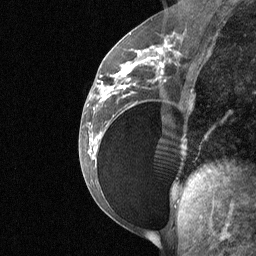
Breast MRI (dynamic contrast-enhanced), one sagittal slice; slice 30 of 64 in the series (ordered by position); dynamic contrast-enhanced study with each time point stored as its own series, time point 2 of 3 at this slice position (early post-contrast, ordered by acquisition time); 1.5 T; TE 4.8 ms, TR 27 ms; 2 mm slice thickness; 256 × 256 image matrix, field of view 200 × 200 mm. Female patient, age 34 years. From the clinical record (not read from this slice): setting: breast cancer imaged before/during neoadjuvant chemotherapy; receptor status: HR-positive, HER2-negative.
Outlined on this slice (semi-automatically segmented with operator editing):
- analysis volume of interest (the breast-tissue region the enhancement analysis was run in; not a lesion): box from (x=92, y=50) to (x=188, y=185) px
- tumour enhancement mask (voxels above the 90 % enhancement threshold inside the analysis volume of interest): (x=99, y=50)–(x=164, y=100)